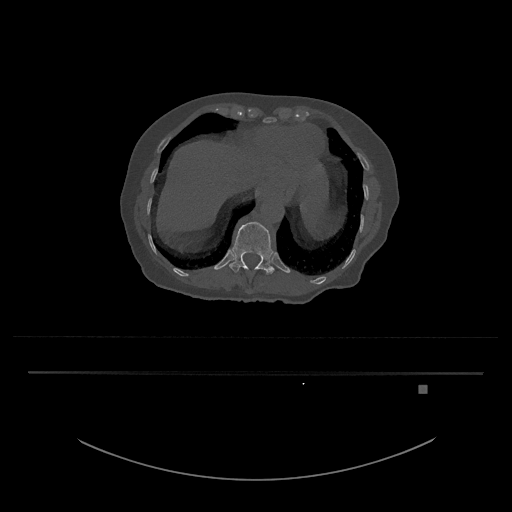
CT including the spine, one axial slice; position 625 of 797 along the scan axis; reconstruction kernel Br40s/3; 120 kVp; bone window (W 1800 / L 400 HU); 512 × 512 image matrix, field of view 500 × 500 mm. Patient: female, 57 years. From the clinical record (not read from this slice): primary cancer: cervical.
Outlined on this slice (semi-automatic segmentation, software-assisted and operator-edited):
- T12 vertebra: box from (x=229, y=222) to (x=274, y=274) px